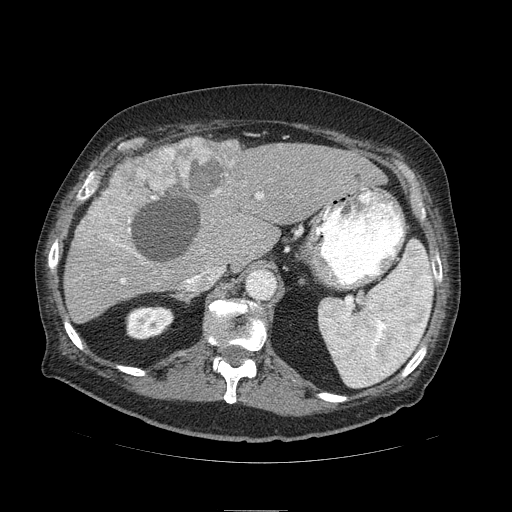
Contrast-enhanced abdominal CT (liver protocol), one axial slice. Reconstruction kernel STANDARD. Soft-tissue window (W 400 / L 40 HU). 2.5 mm slice thickness. 512 × 512 image matrix, field of view 440 × 440 mm. From the clinical record (not read from this slice): diagnosis: hepatocellular carcinoma (patient treated with transarterial chemoembolisation; whether this scan precedes or follows treatment is not stated here); TNM stage (as recorded): Stage-IIIA; Child-Pugh class: B.
Outlined on this slice (semi-automatic segmentation, software-assisted and operator-edited):
- liver parenchyma outside the tumour (the mass and vessels are separate outlines, so this box may not span the whole liver): bounding box [x1, y1, x2, y2] px = [64, 140, 384, 322]
- mass: [78, 137, 243, 250]
- liver vessels: [121, 194, 263, 283]